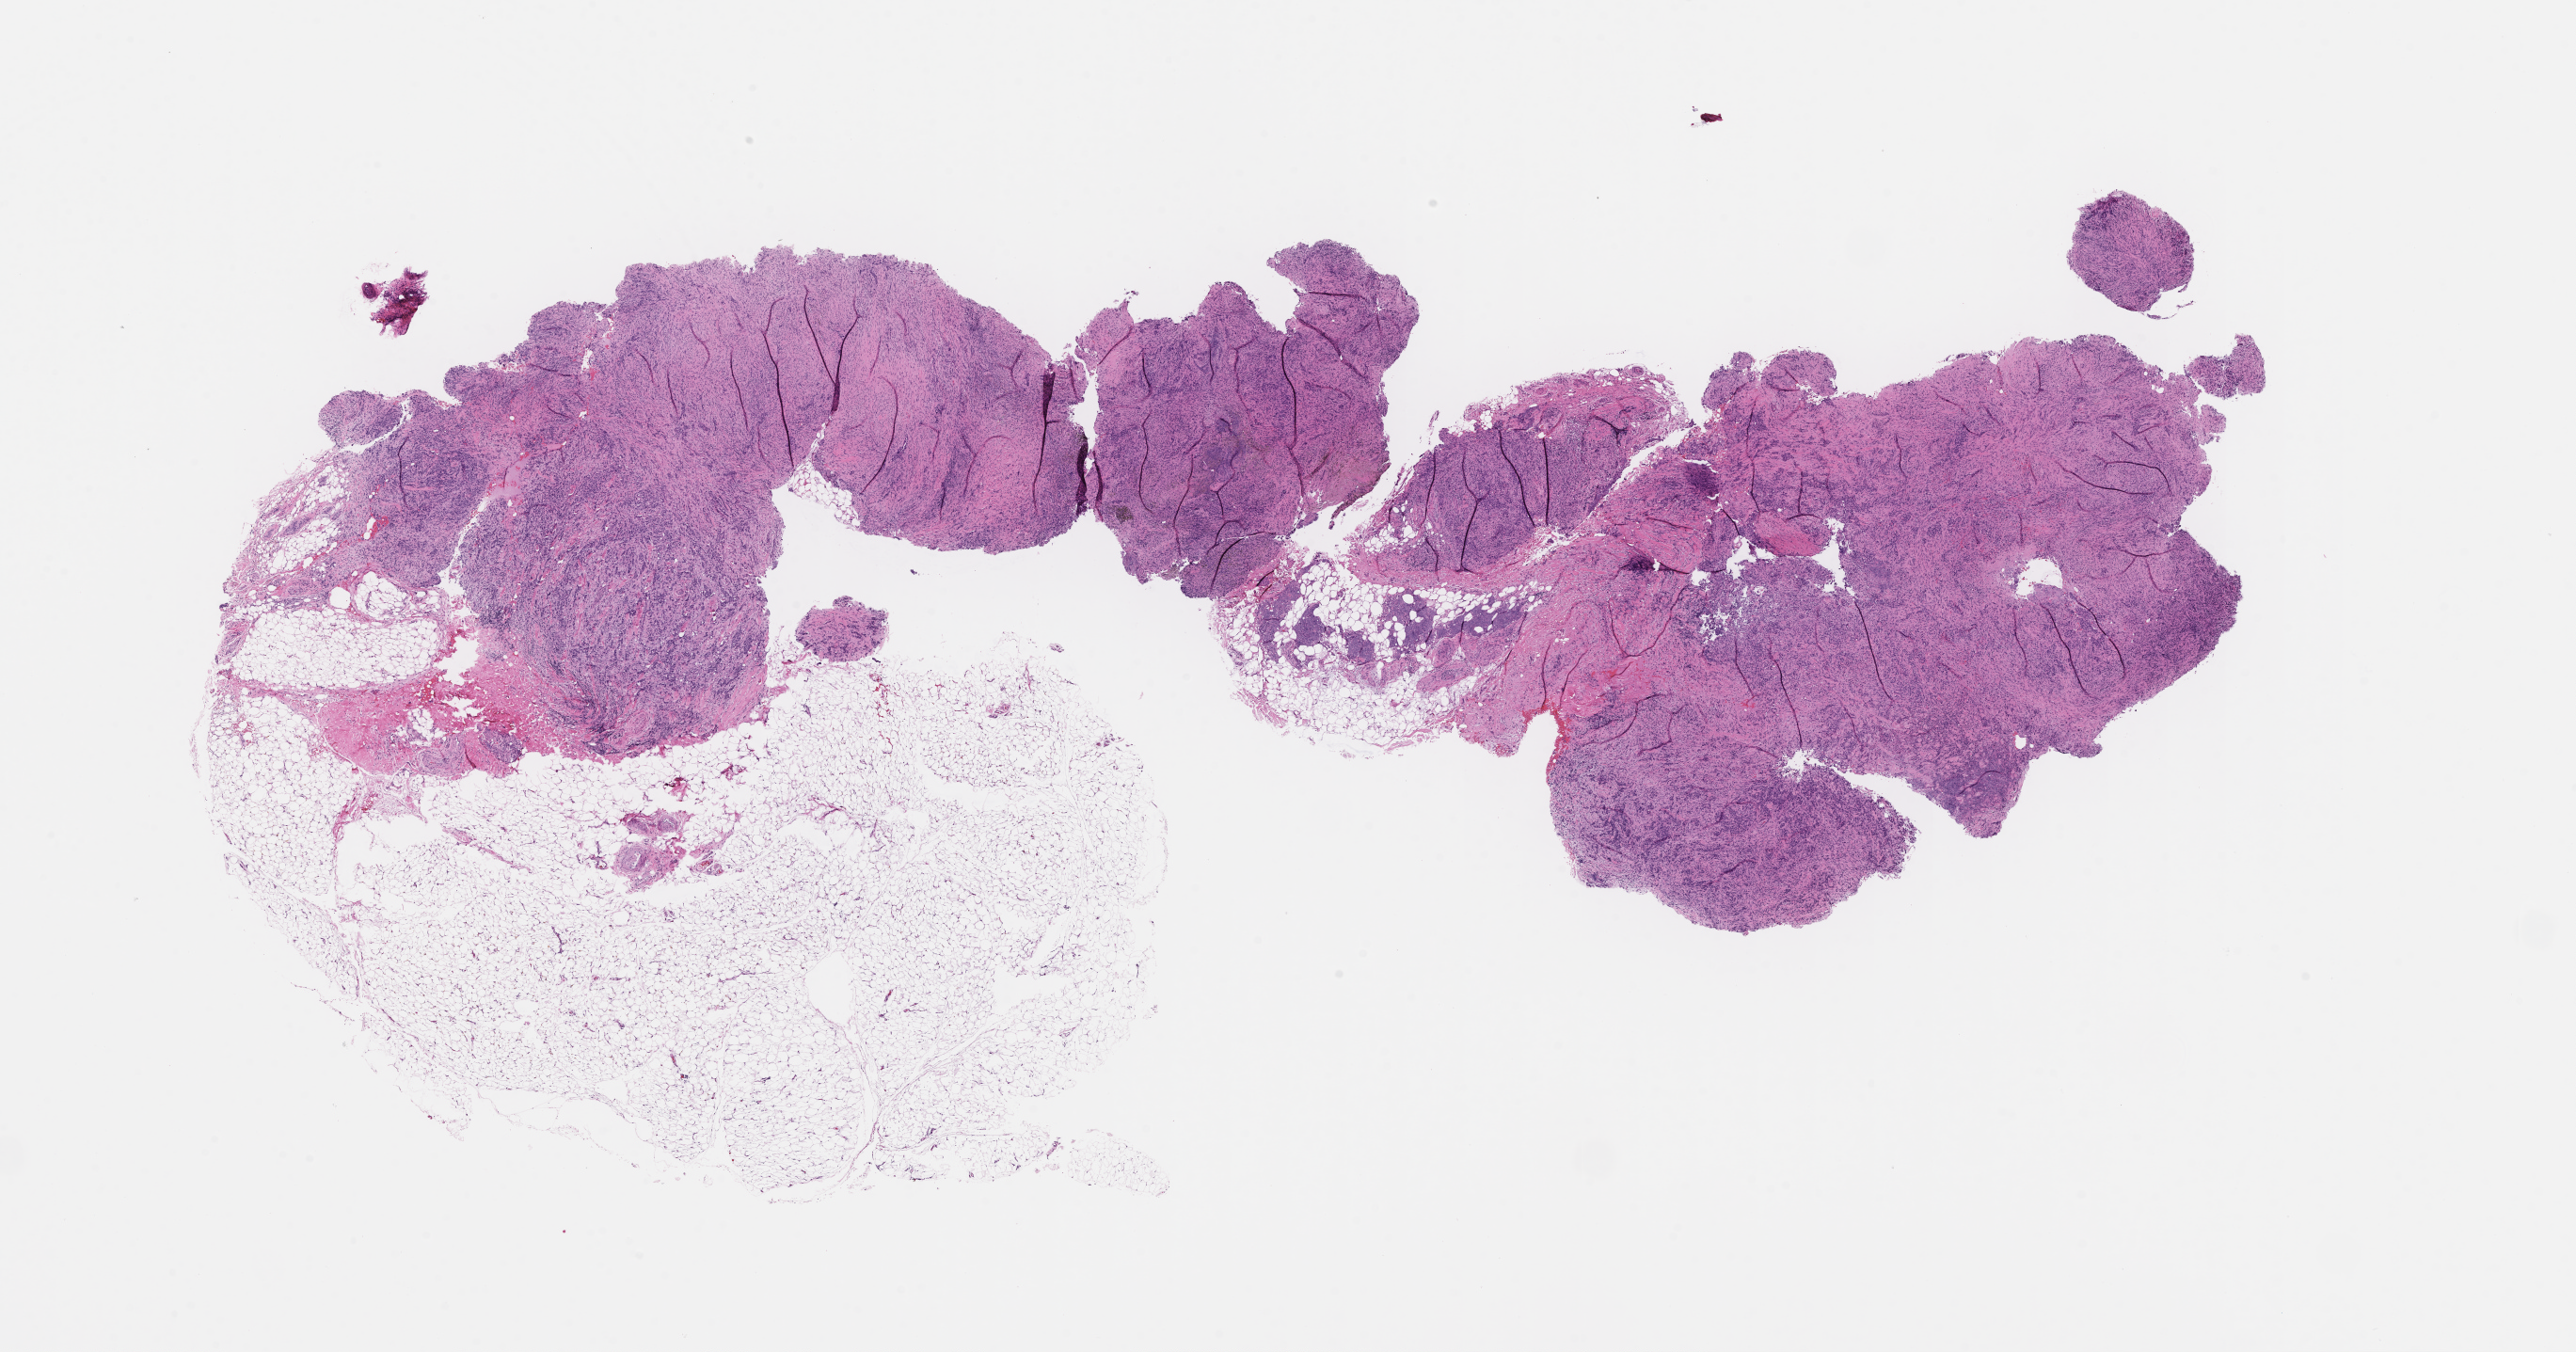
H&E whole-slide image — whole scanned area (about 22.1 x 11.6 mm) shown as a low-resolution overview; formalin-fixed, paraffin-embedded (FFPE) tissue. Patient sex: female.
This section: metastatic tumor tissue. Primary diagnosis of the patient: Non-Small Cell Lung Carcinoma.